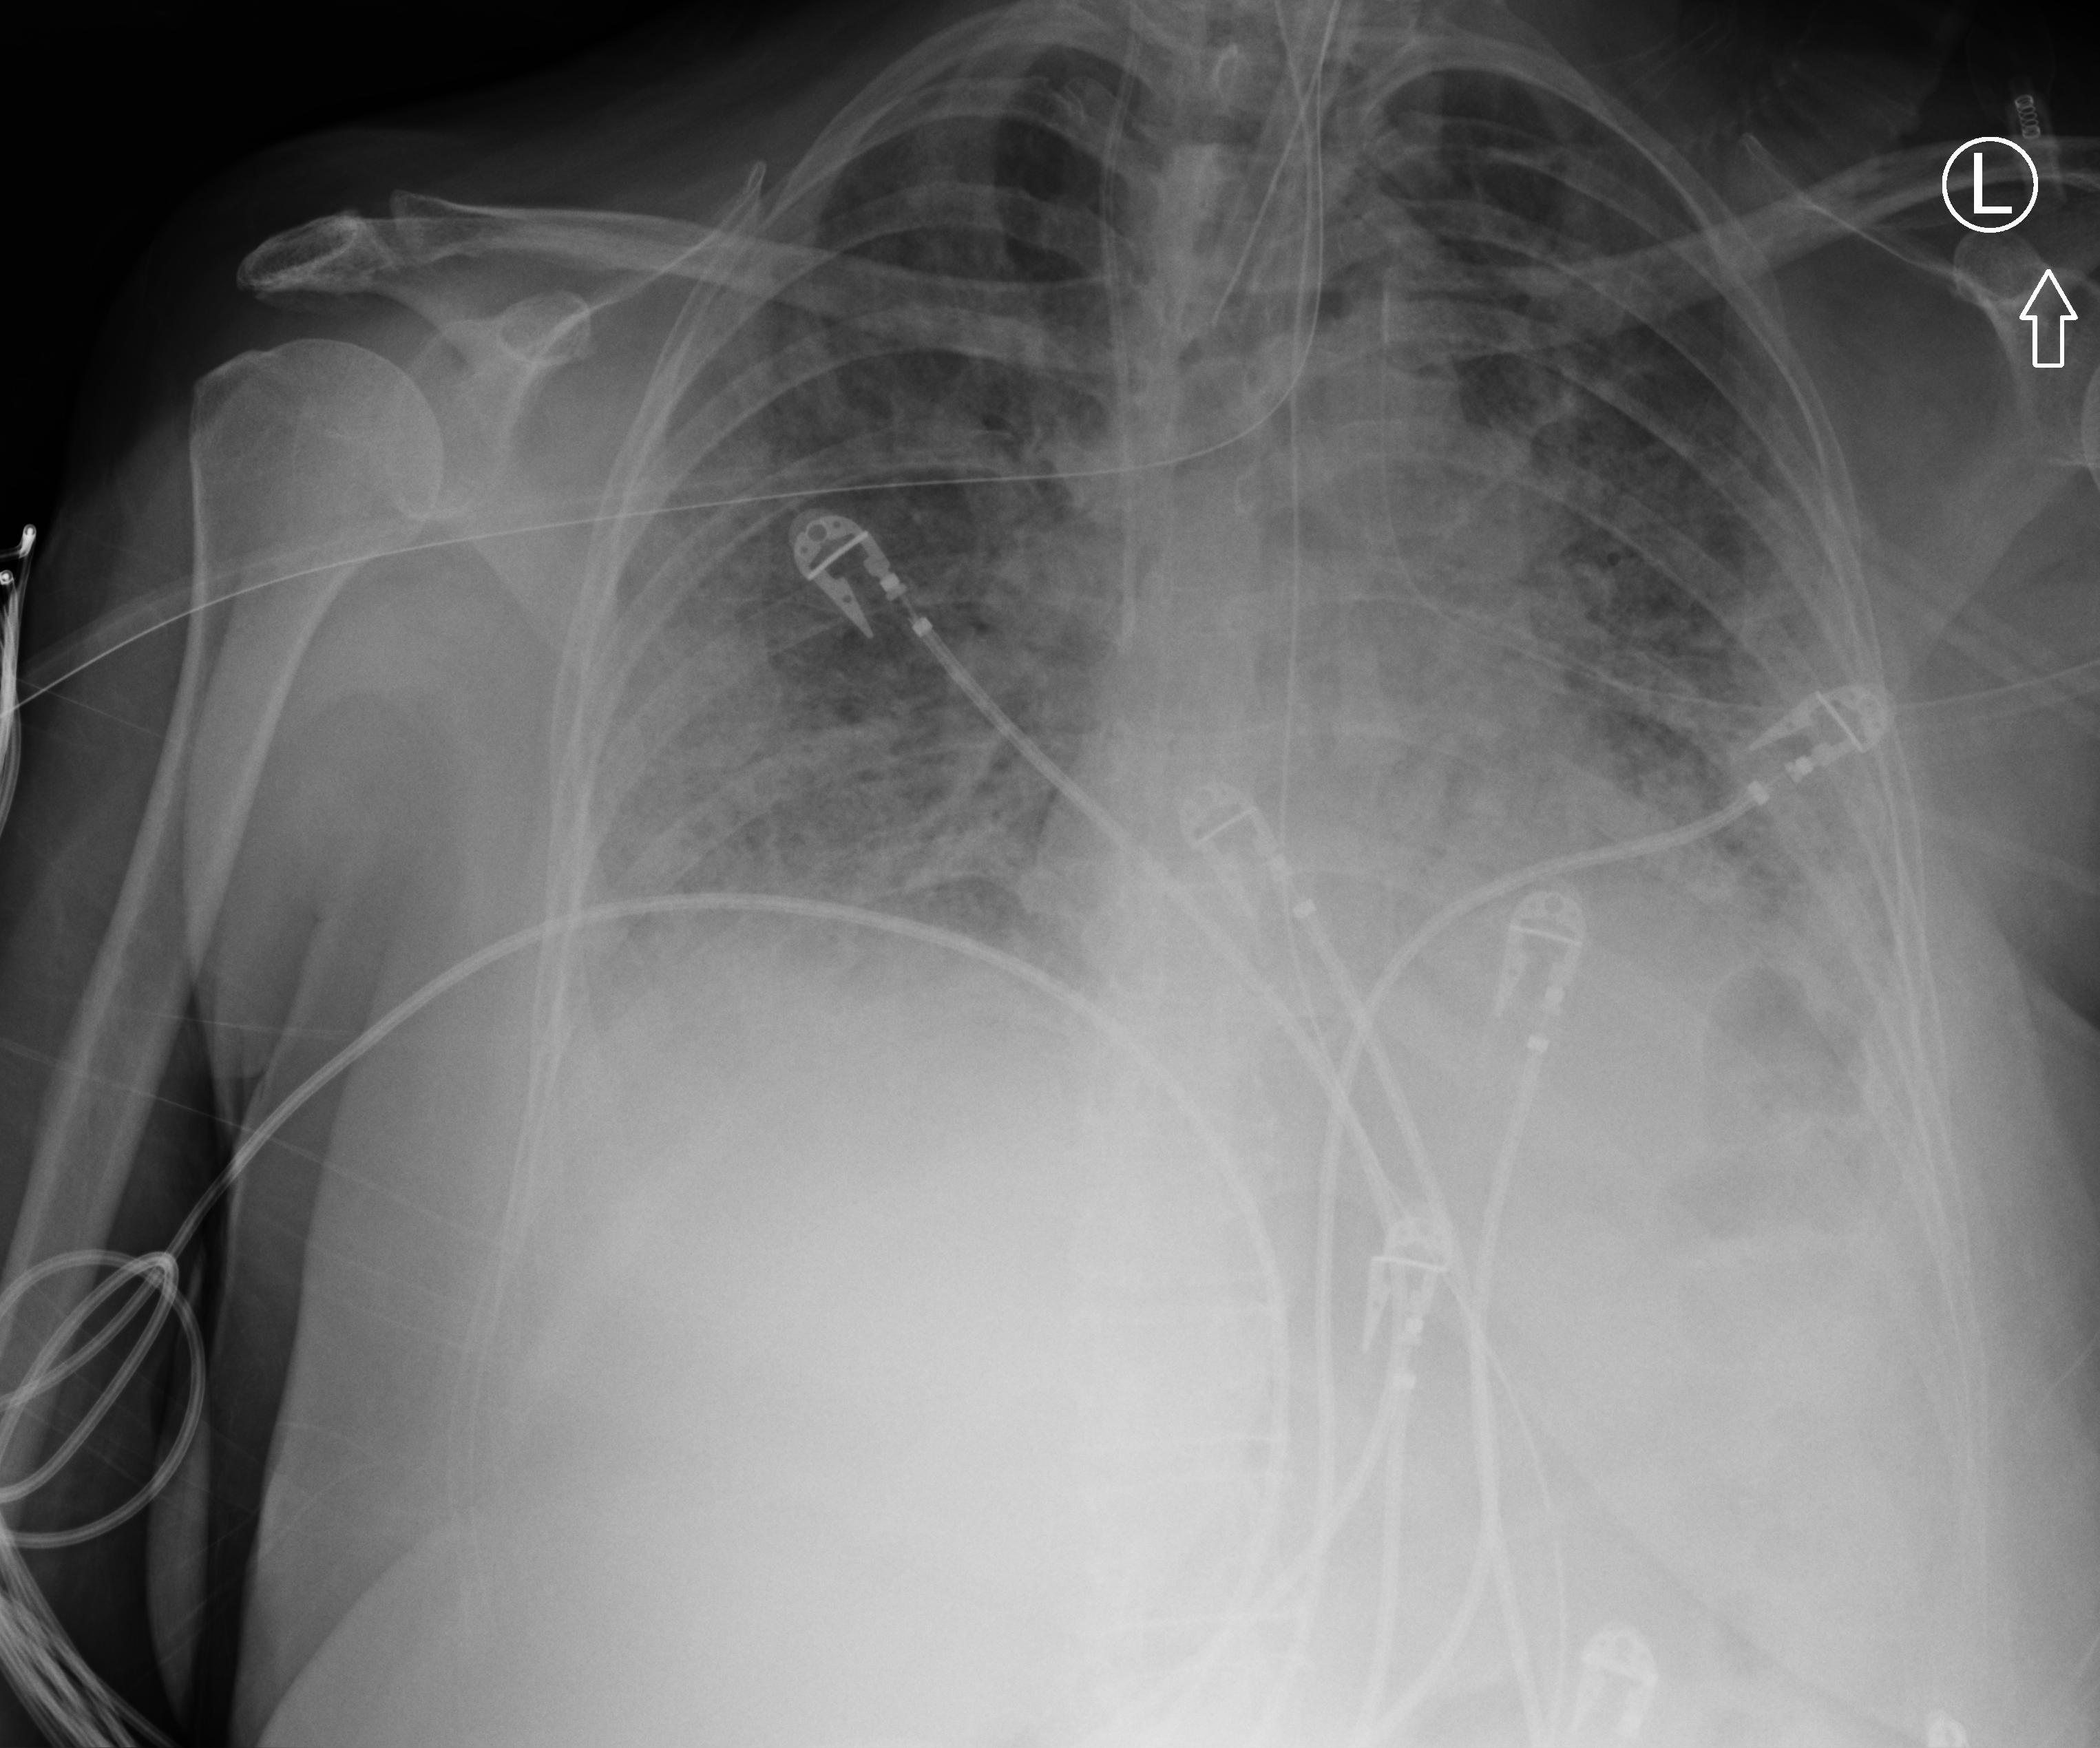
Portable chest radiograph, anteroposterior (AP) projection. Patient hospitalised with COVID-19; female, aged 60–74 years.
Hospital-stay facts (about this admission, not read from this image; timing relative to this image not recorded):
- admitted to intensive care during this hospital stay: yes
- chronic kidney disease (admission record): no
- mechanically ventilated during this hospital stay: yes